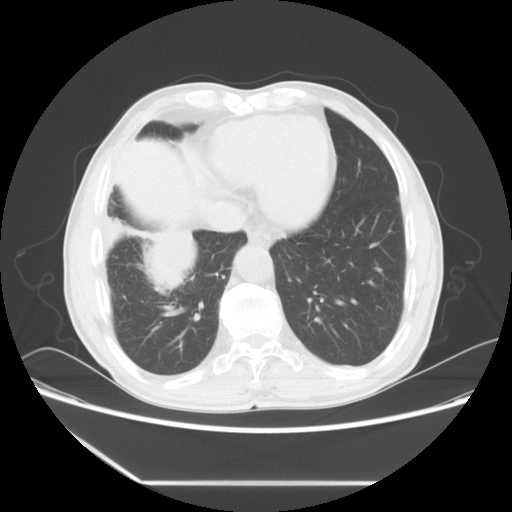
Chest CT, one axial slice; position 19 of 60 along the scan axis; 120 kVp; lung window (W 1500 / L -600 HU); 5 mm slice thickness; 512 × 512 image matrix, field of view 386 × 386 mm. Patient: male, 72 years. From the clinical record (not read from this slice): clinical TNM (as recorded): T1c N0 M0.
Outlined on this slice (bounding box drawn by a radiologist):
- lung tumour (recorded histology: squamous cell carcinoma): box from (x=109, y=212) to (x=204, y=301) px